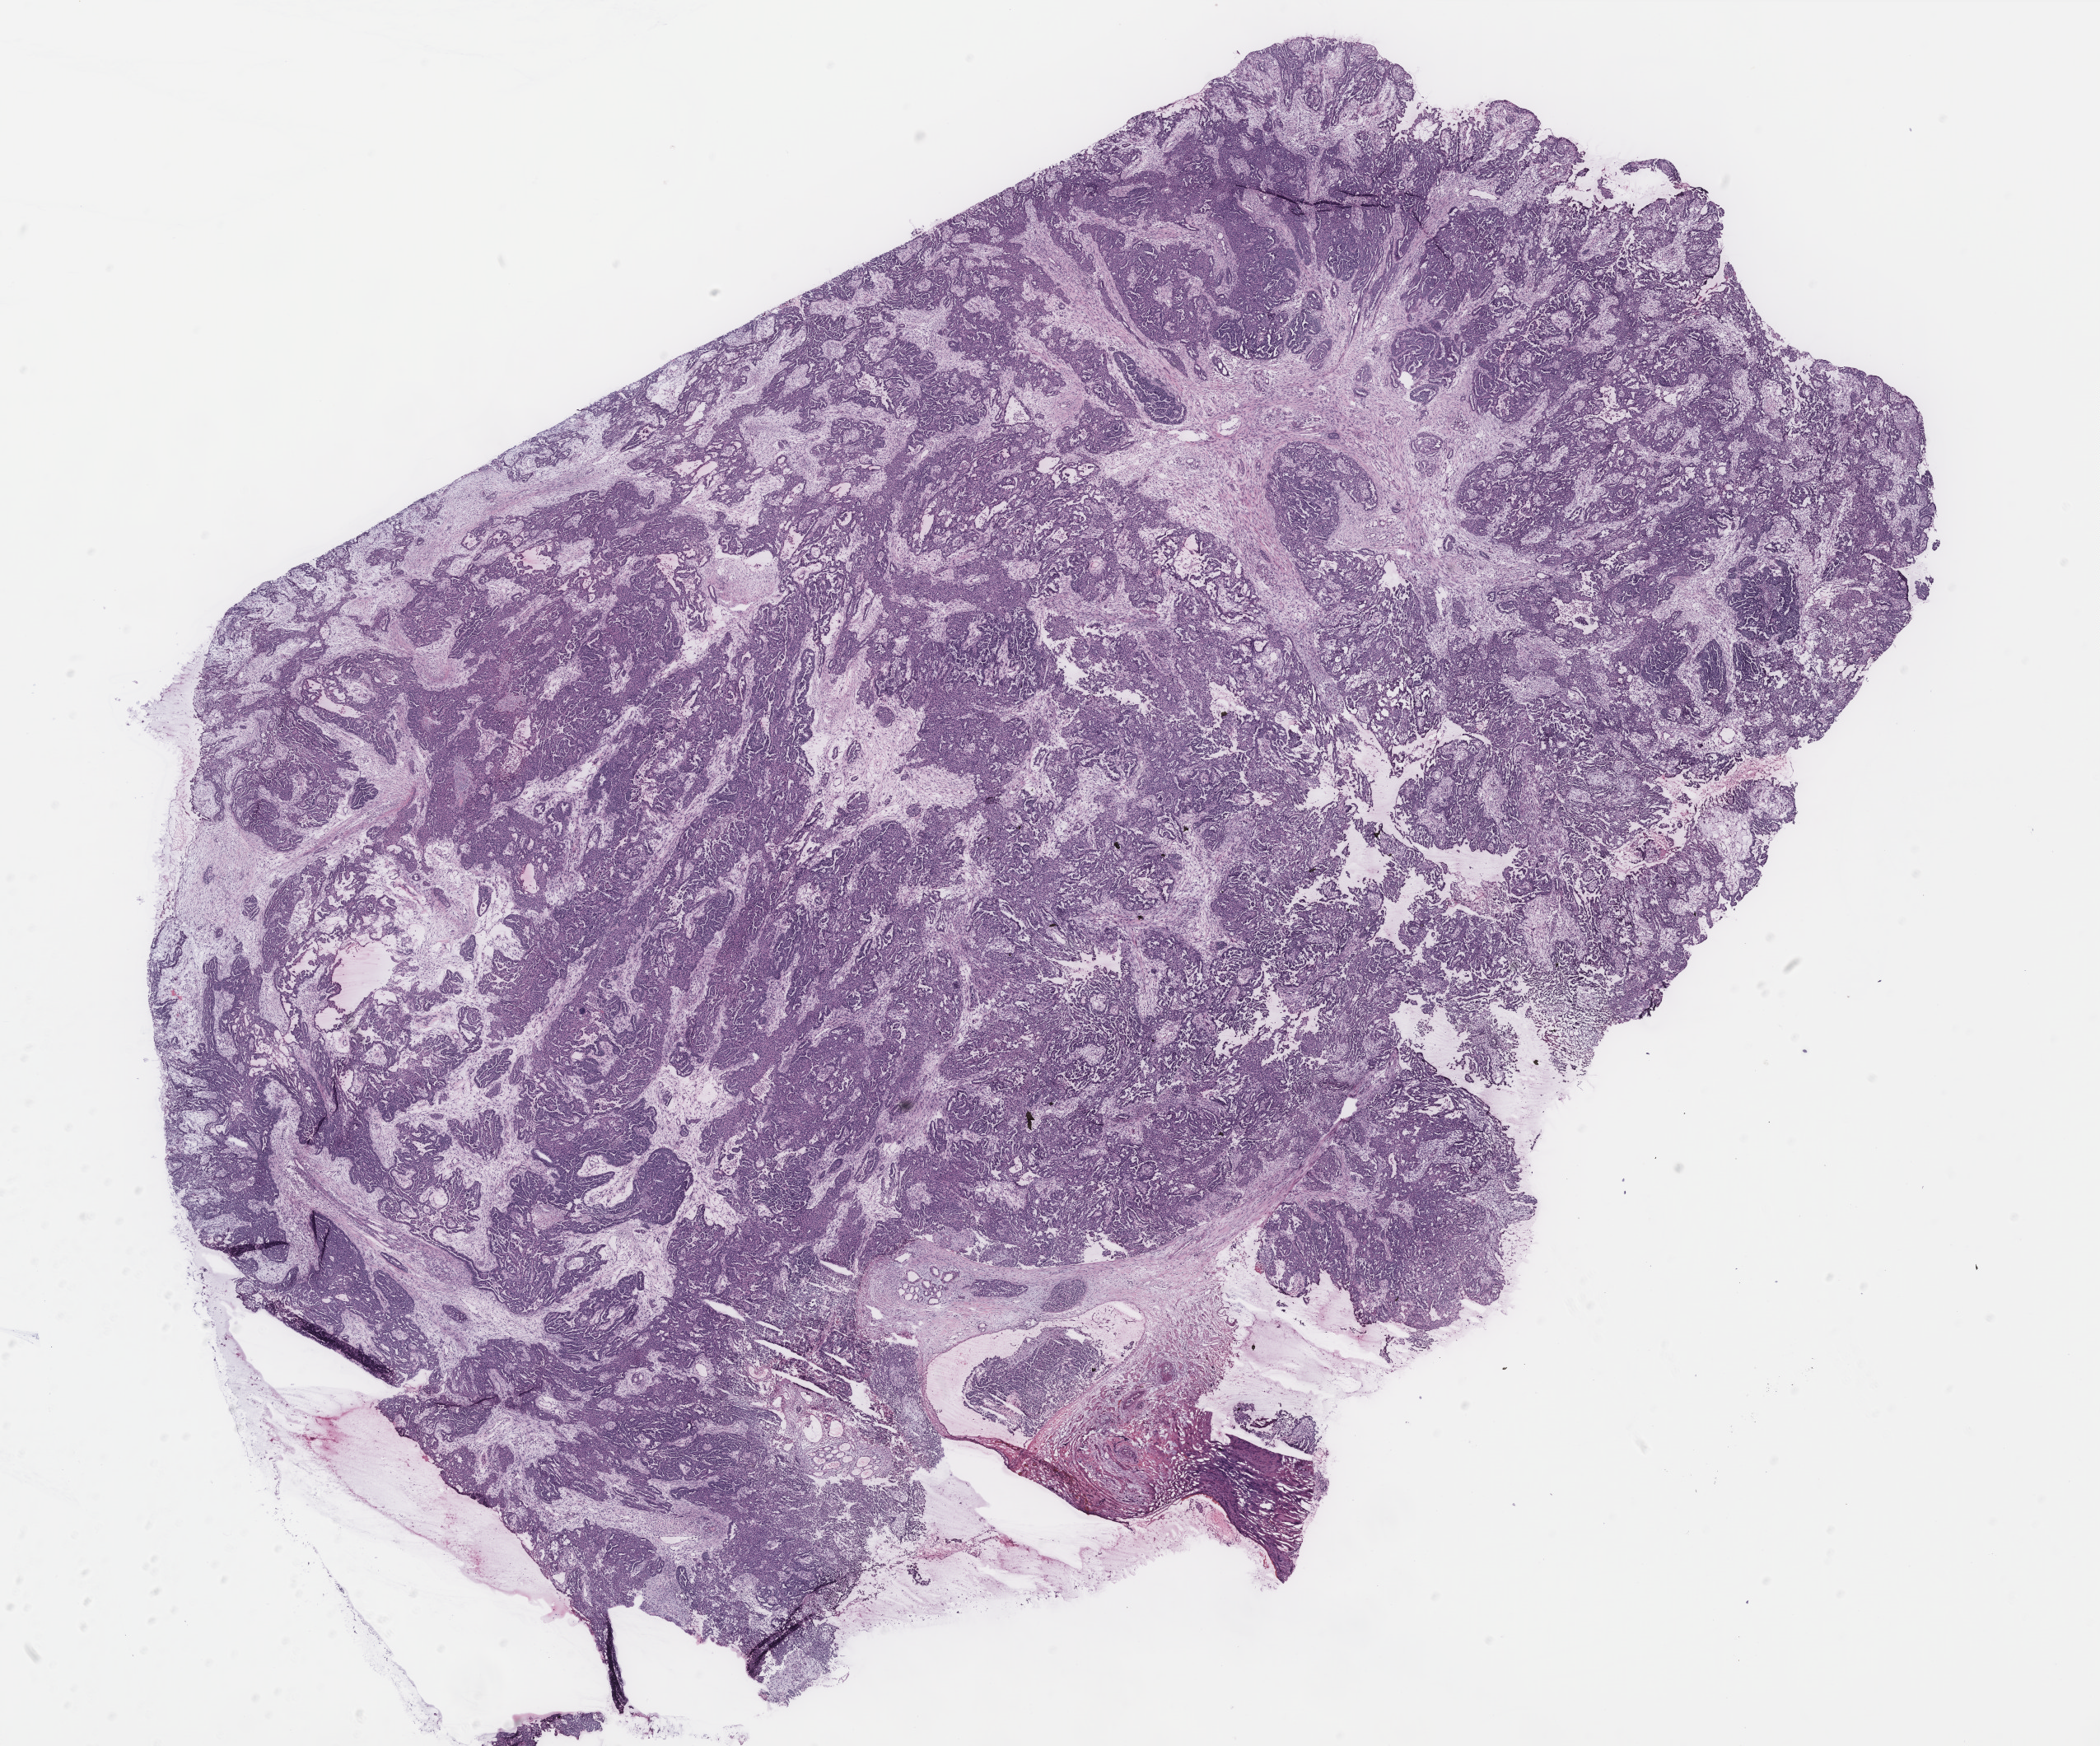
Whole-slide histology image, H&E — whole scanned area (about 20.4 x 17.0 mm, slide scanned at 40x) shown as a low-resolution overview; ovary, tumour tissue. 50-year-old female patient.
Primary tumour site (as recorded): ovary. Histologic diagnosis: Serous adenocarcinoma, NOS.